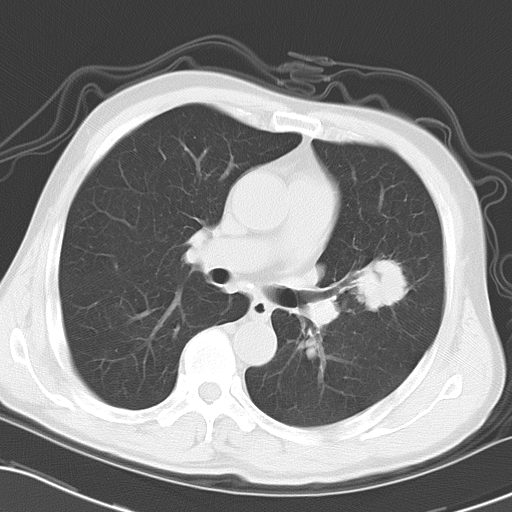
Chest CT, one axial slice; slice 15 of 27 in the series (ordered by position); 120 kVp; lung window (W 1500 / L -600 HU); 10 mm slice thickness; 512 × 512 image matrix, field of view 318 × 318 mm. Patient: male, 60 years. From the clinical record (not read from this slice): clinical TNM (as recorded): T1c N1 M0.
Structures marked on this image (rectangle marked by the reading radiologist):
- lung tumour (recorded histology: adenocarcinoma): bounding box [x1, y1, x2, y2] px = [350, 248, 413, 315]
- lung tumour (recorded histology: adenocarcinoma): [352, 244, 422, 321]